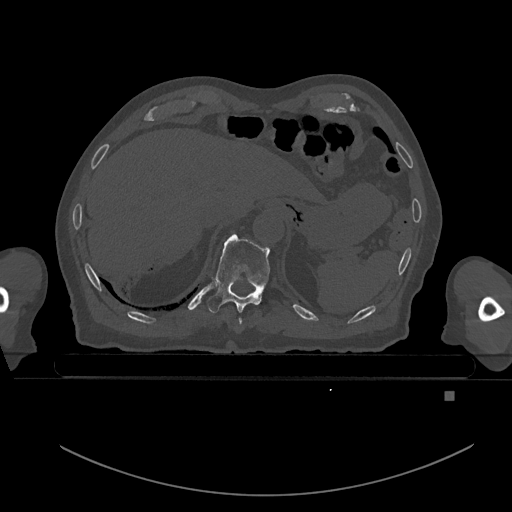
CT including the spine, one axial slice; position 89 of 969 along the scan axis; bone window (W 1800 / L 400 HU); 0.5 mm slice thickness; 512 × 512 image matrix, field of view 456 × 456 mm. Patient: male, 82 years. Case-level facts recorded for this patient, not image findings: primary cancer: prostate; vertebrae with lytic lesions (as recorded): T11, T9, T8, T2.
Outlined on this slice (semi-automatic segmentation, software-assisted and operator-edited):
- T10 vertebra: box from (x=207, y=234) to (x=270, y=313) px
- T9 vertebra: (x=238, y=318)–(x=242, y=325)